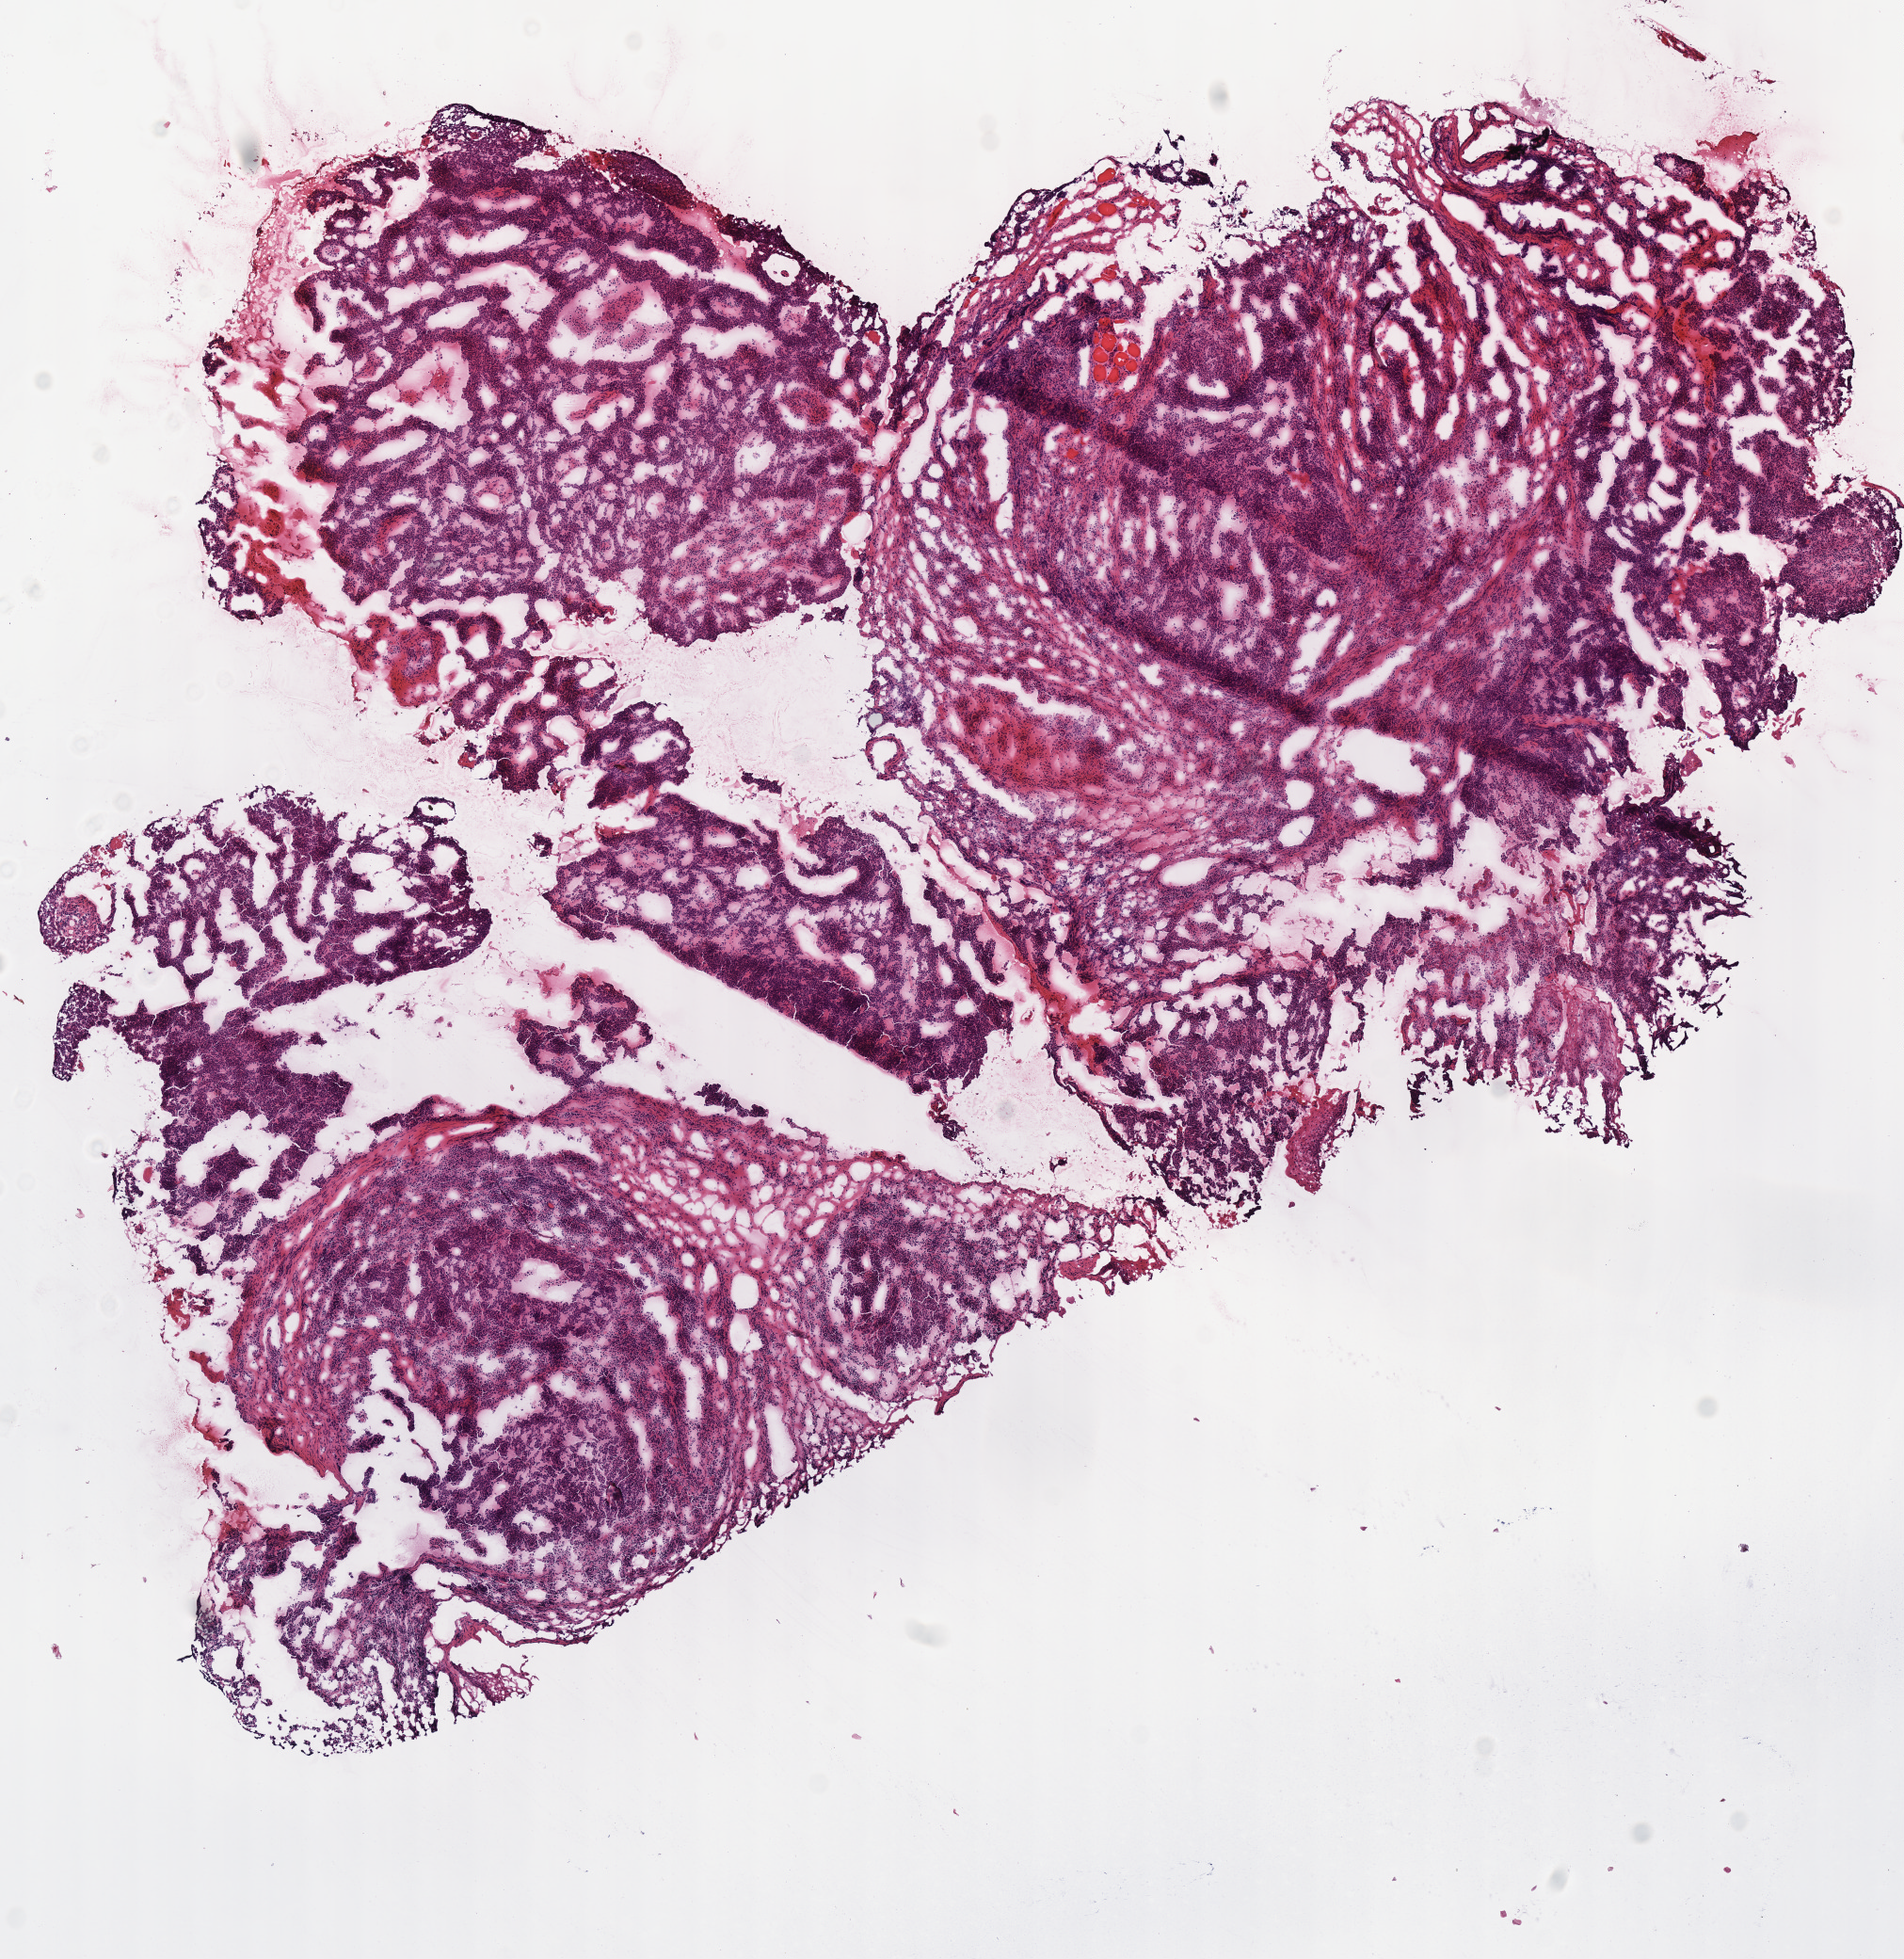
Whole-slide histology image, Hematoxylin and eosin (H&E) stained — whole scanned area (about 8.0 x 8.2 mm) shown as a low-resolution overview, frozen section from the top of the tissue portion, head and neck, primary tumour sample. Male, age 62 years at initial diagnosis. Histologic grade: G4 (undifferentiated). Pathologist review of this section (percent, as recorded): tumour cells 85%, tumour nuclei 85%, normal cells 0%, stromal cells 15%, necrosis 0%. Inflammatory infiltration, as recorded: lymphocyte infiltration 10%.
- histologic diagnosis: Squamous cell carcinoma, NOS (base of tongue, NOS)
- laterality: left